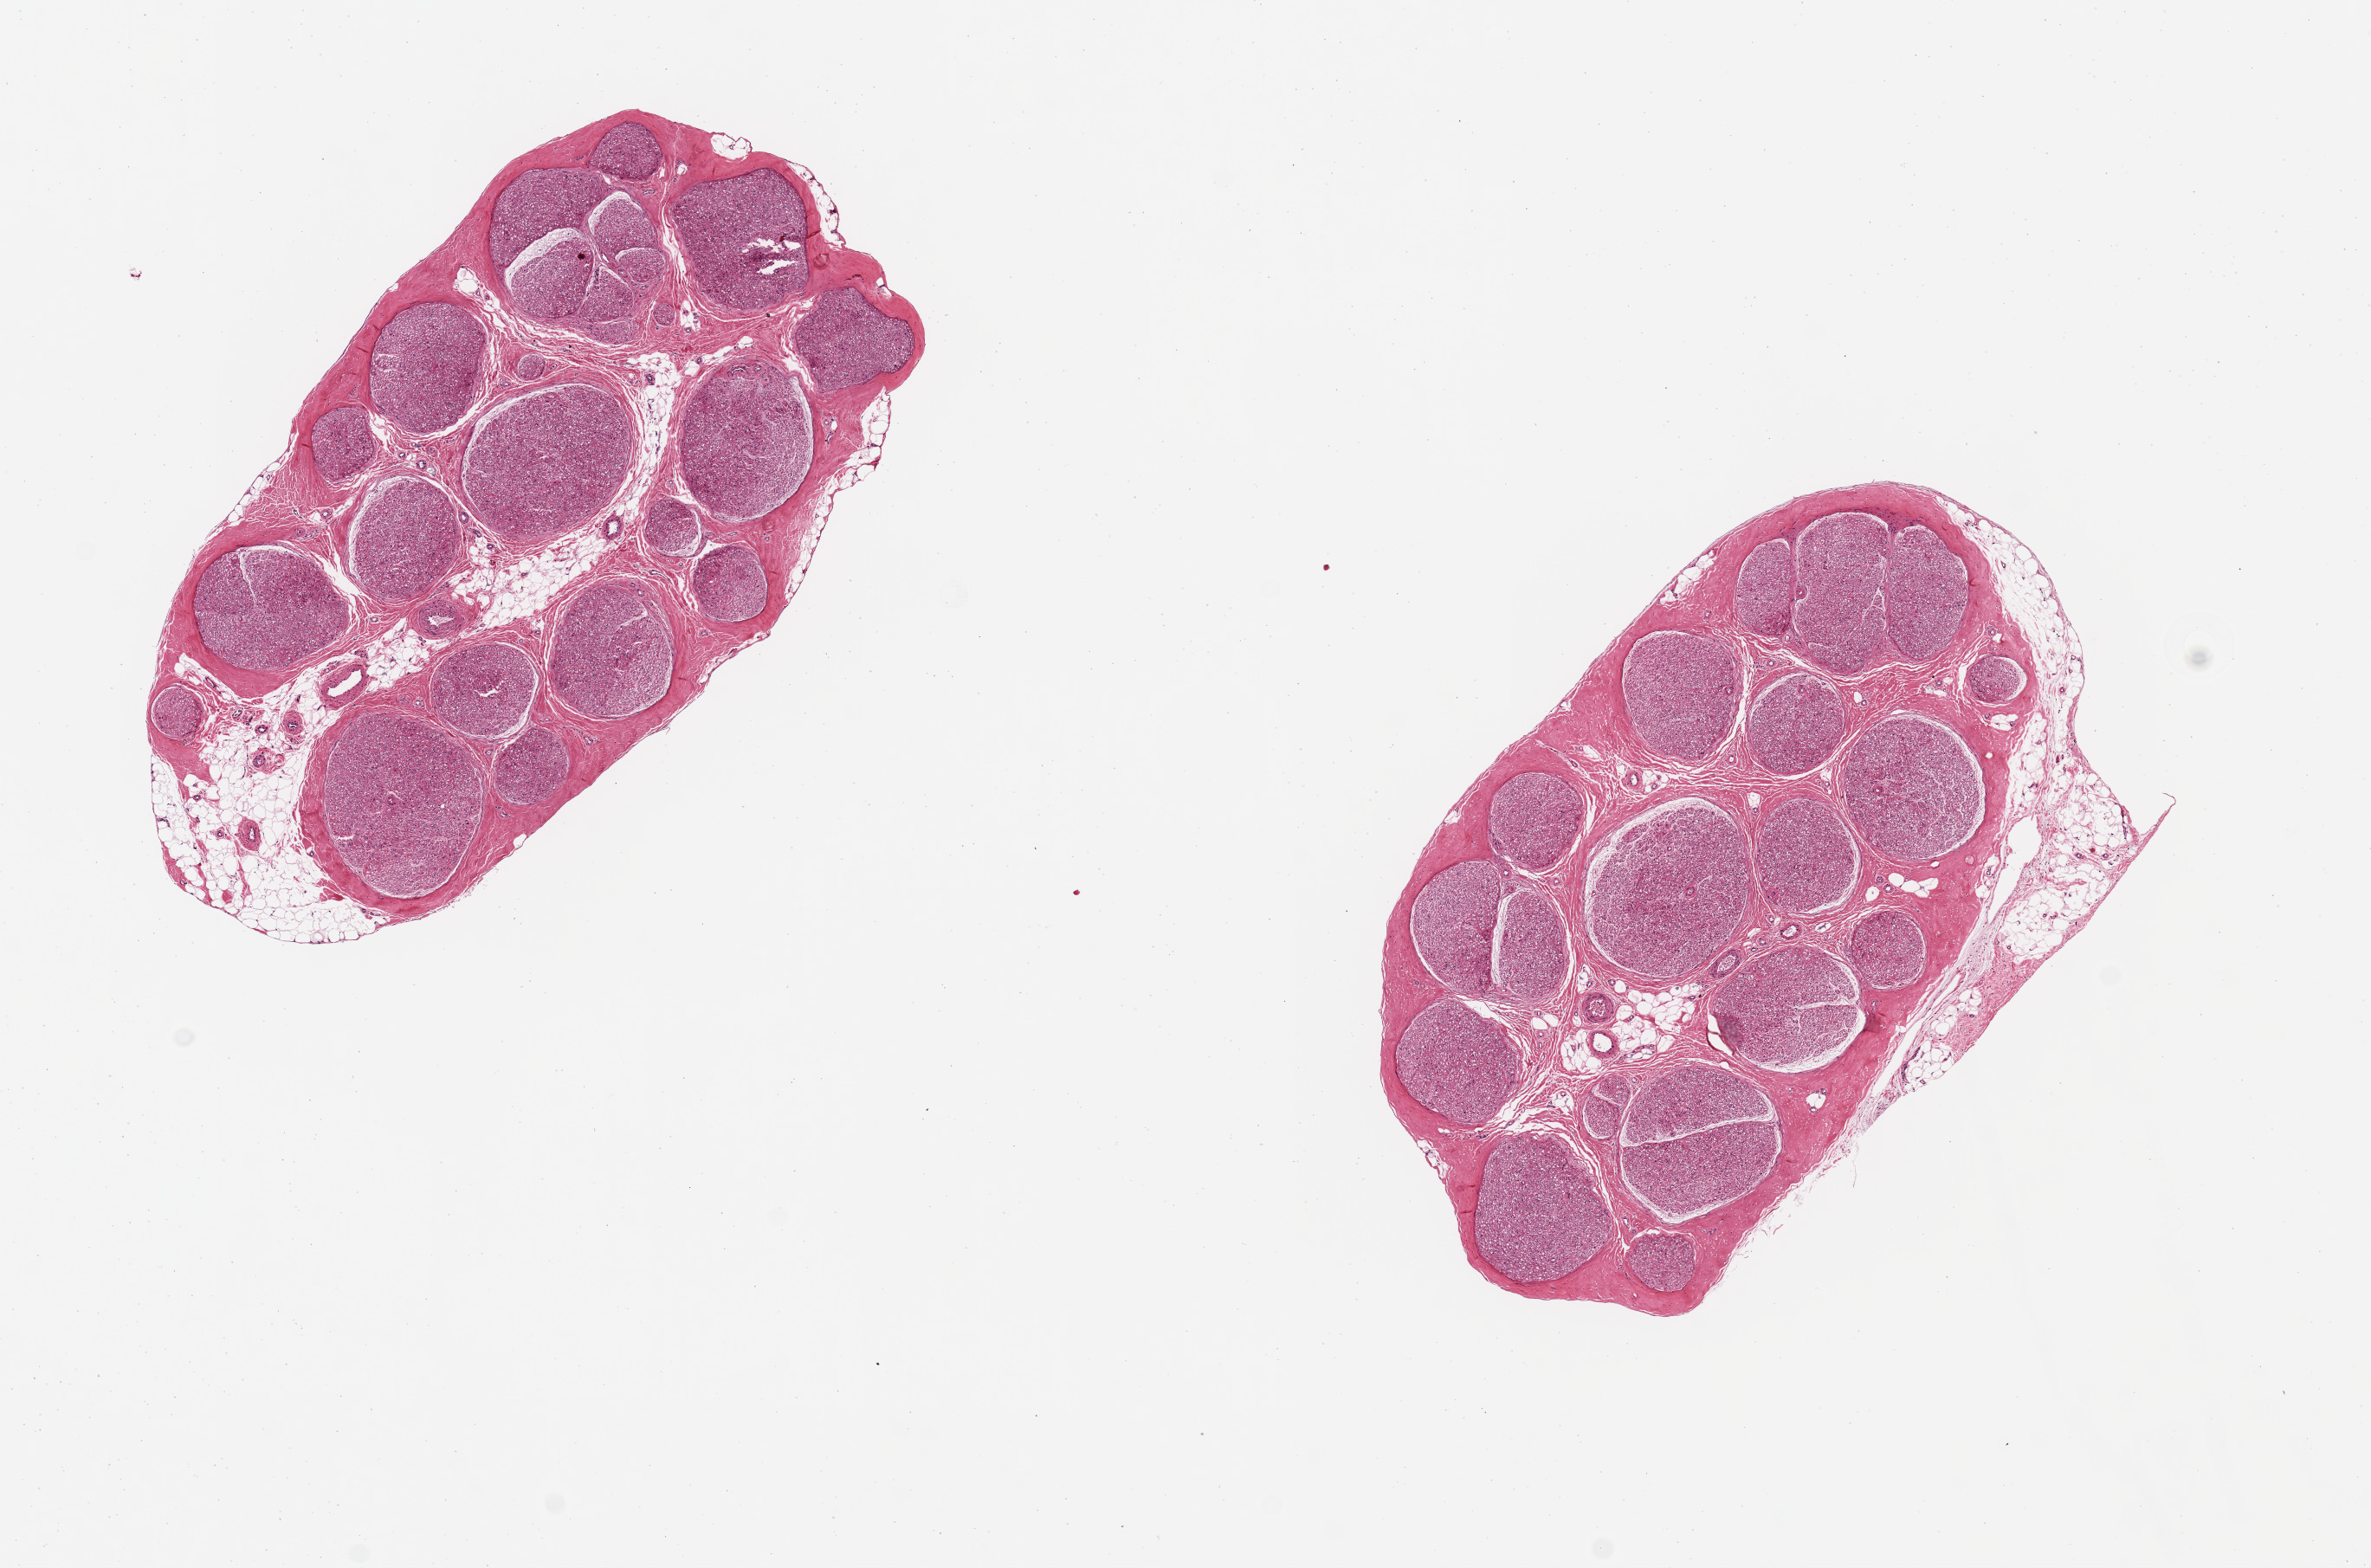
Whole-slide image, hematoxylin and eosin (H&E) stain, a low-resolution overview of the entire scanned area, about 10.8 x 7.2 mm; PAXgene-fixed paraffin-embedded (PFPE) section; target tissue: tibial nerve; donor tissue sample. Donor sex: male.
Review note (as recorded): 2 ~4.3x2.3mm aliquots; peripheral fat is ~10% of specimen (focally ~0.5mm).